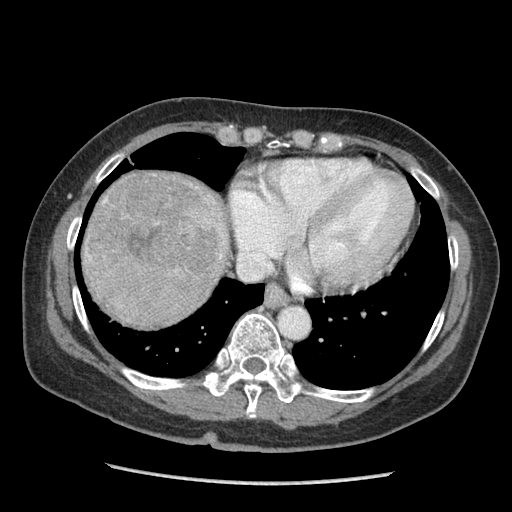
Contrast-enhanced abdominal CT (liver protocol), one axial slice; position 87 of 105 along the scan axis; reconstruction kernel STANDARD; soft-tissue window (W 400 / L 40 HU); 512 × 512 image matrix. From the clinical record (not read from this slice): diagnosis: hepatocellular carcinoma (patient treated with transarterial chemoembolisation; whether this scan precedes or follows treatment is not stated here); TNM stage (as recorded): Stage-I.
Annotated regions visible in this slice (semi-automatic segmentation, software-assisted and operator-edited):
- liver parenchyma outside the tumour (the mass and vessels are separate outlines, so this box may not span the whole liver): box from (x=82, y=170) to (x=226, y=324) px
- mass: (x=86, y=174)–(x=231, y=328)